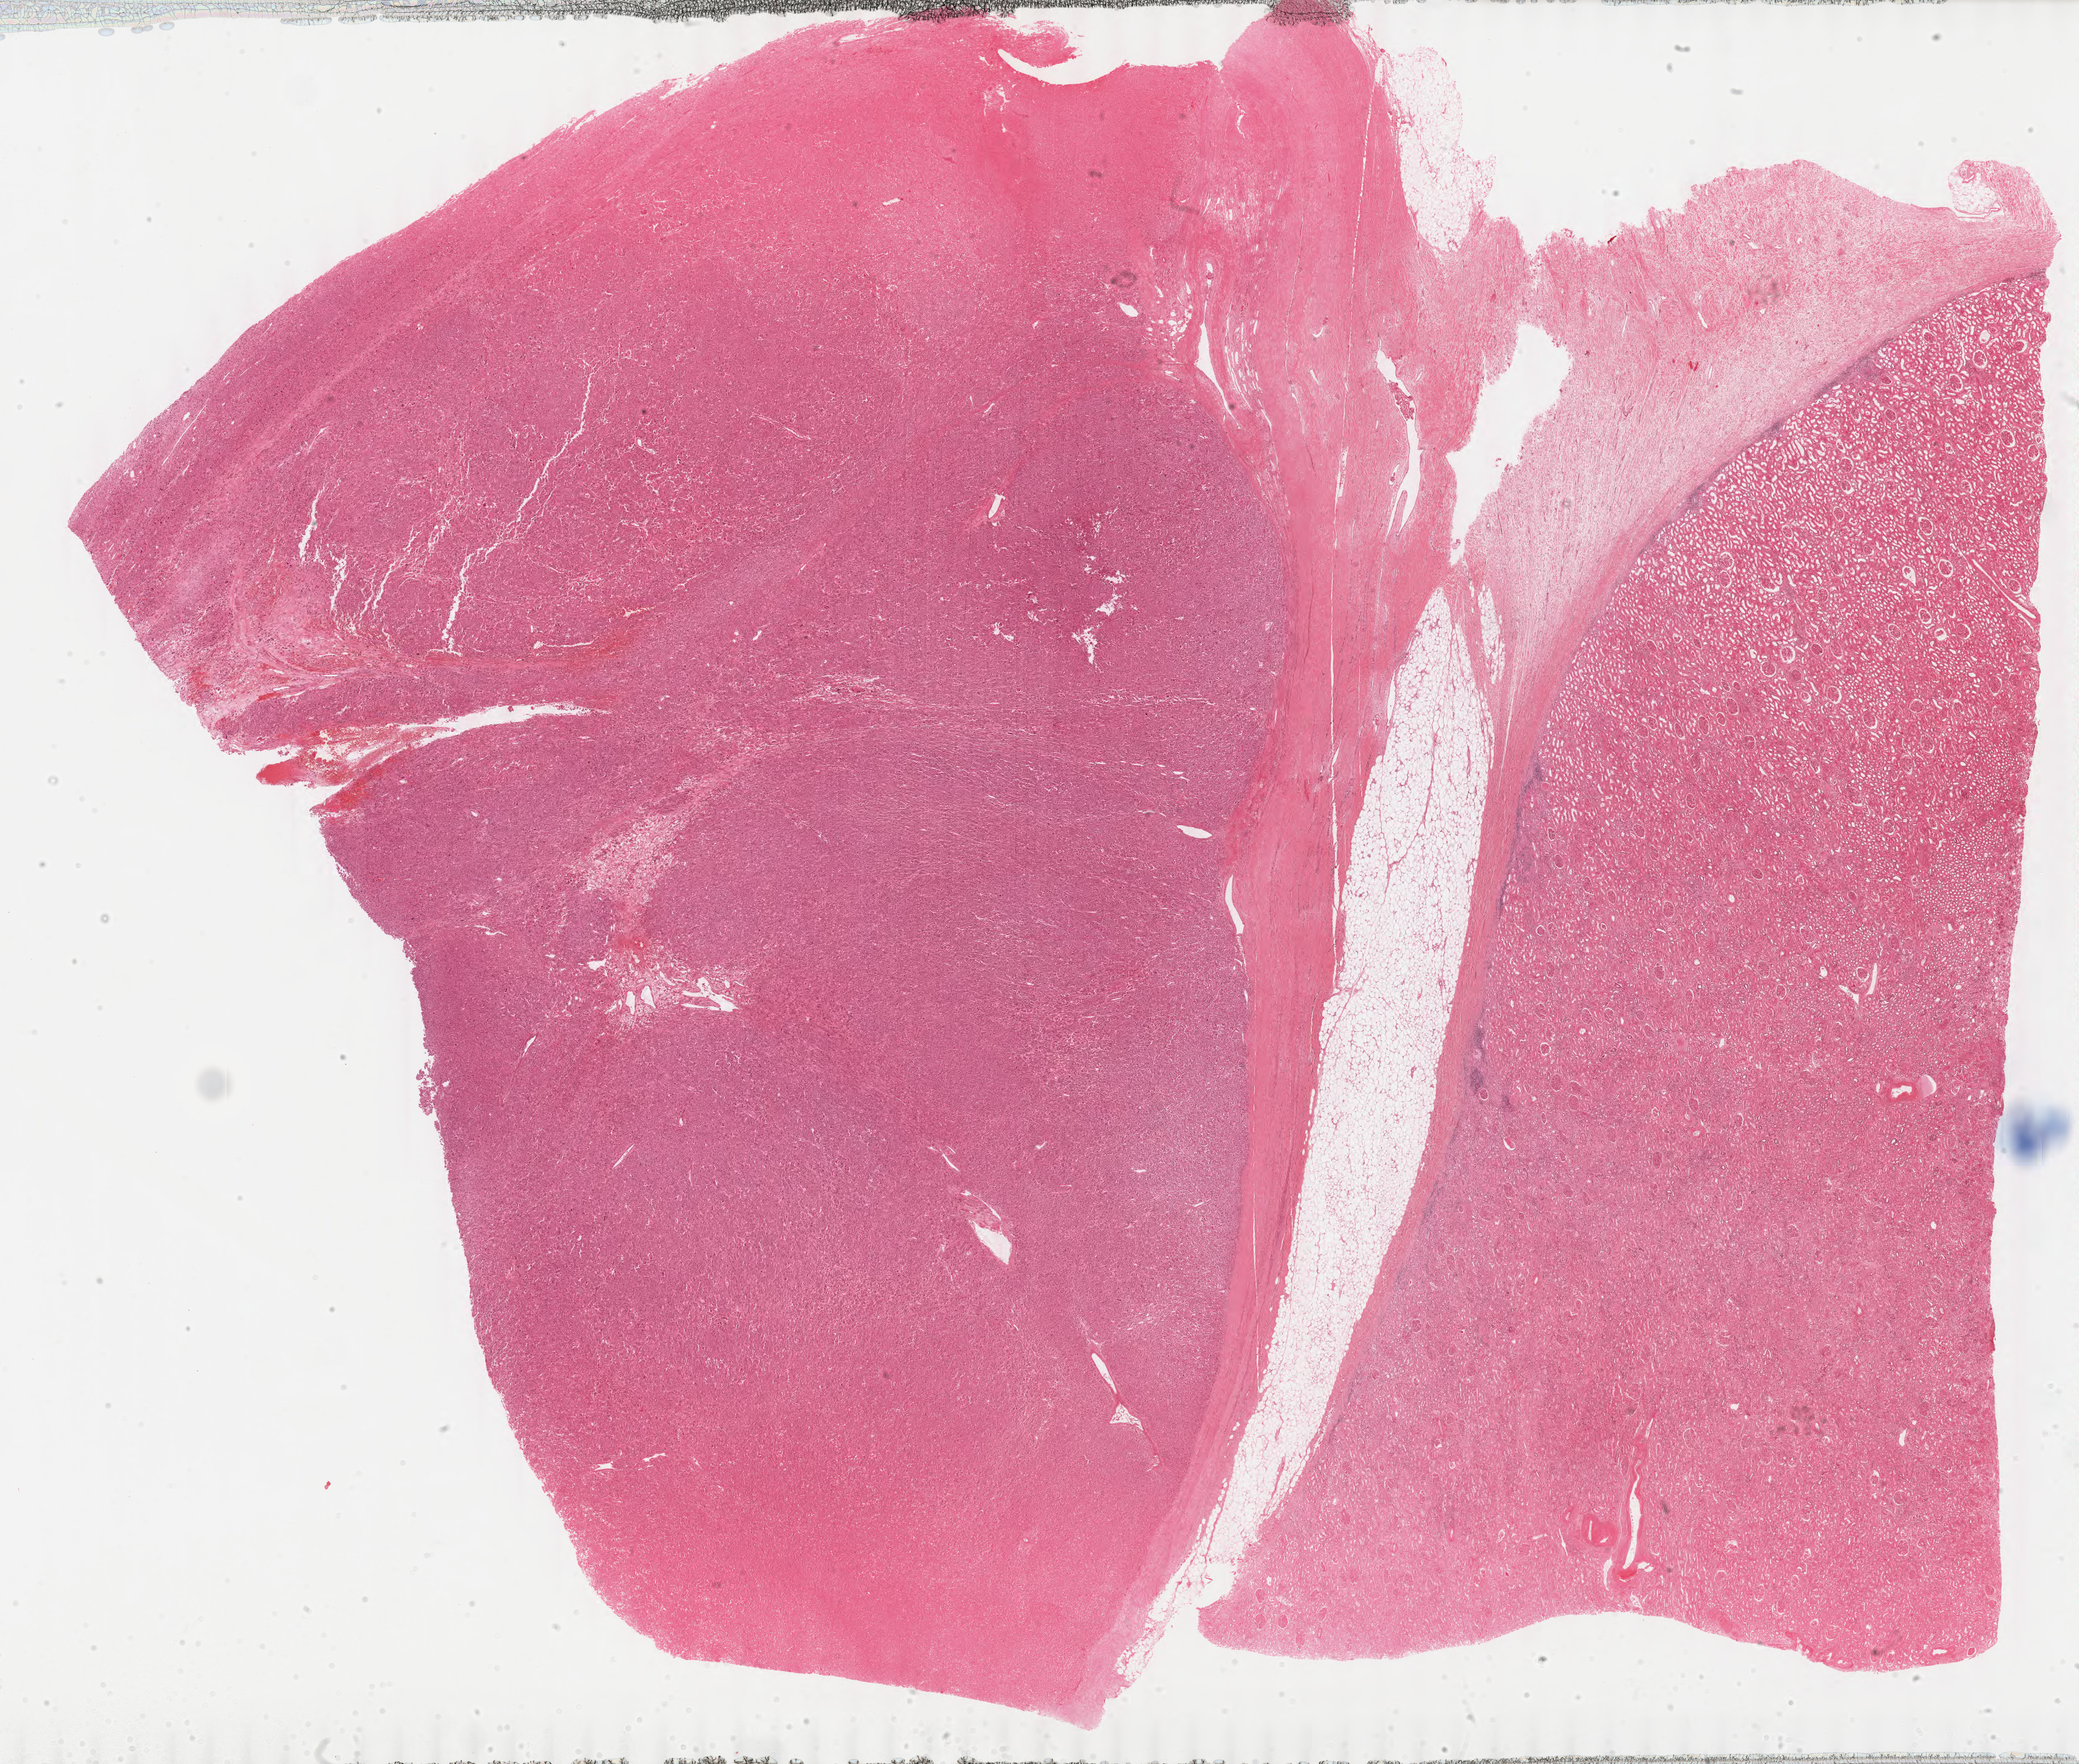
Digitized Hematoxylin and eosin (H&E) stained tissue section (whole slide), low-resolution overview of the scanned area, about 27.0 x 22.9 mm (slide scanned at 40x). FFPE section. Sample: primary tumour, adrenal cortex. Male patient; age at initial diagnosis 63 years.
Diagnosis: Adrenal cortical carcinoma (cortex of adrenal gland).